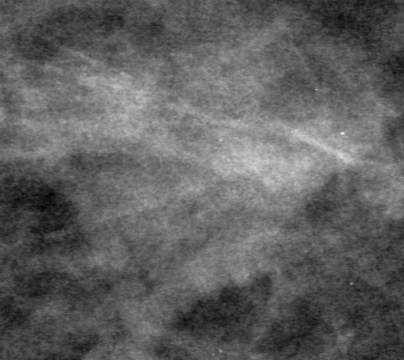
Region of interest cut from a scanned film mammogram (one marked finding); left breast; CC view.
Mass, shape lobulated, margins obscured; BI-RADS assessment category 0 (incomplete: needs additional imaging); subtlety rating 4 on a 1 (subtle) to 5 (obvious) scale; pathology (as recorded): benign.